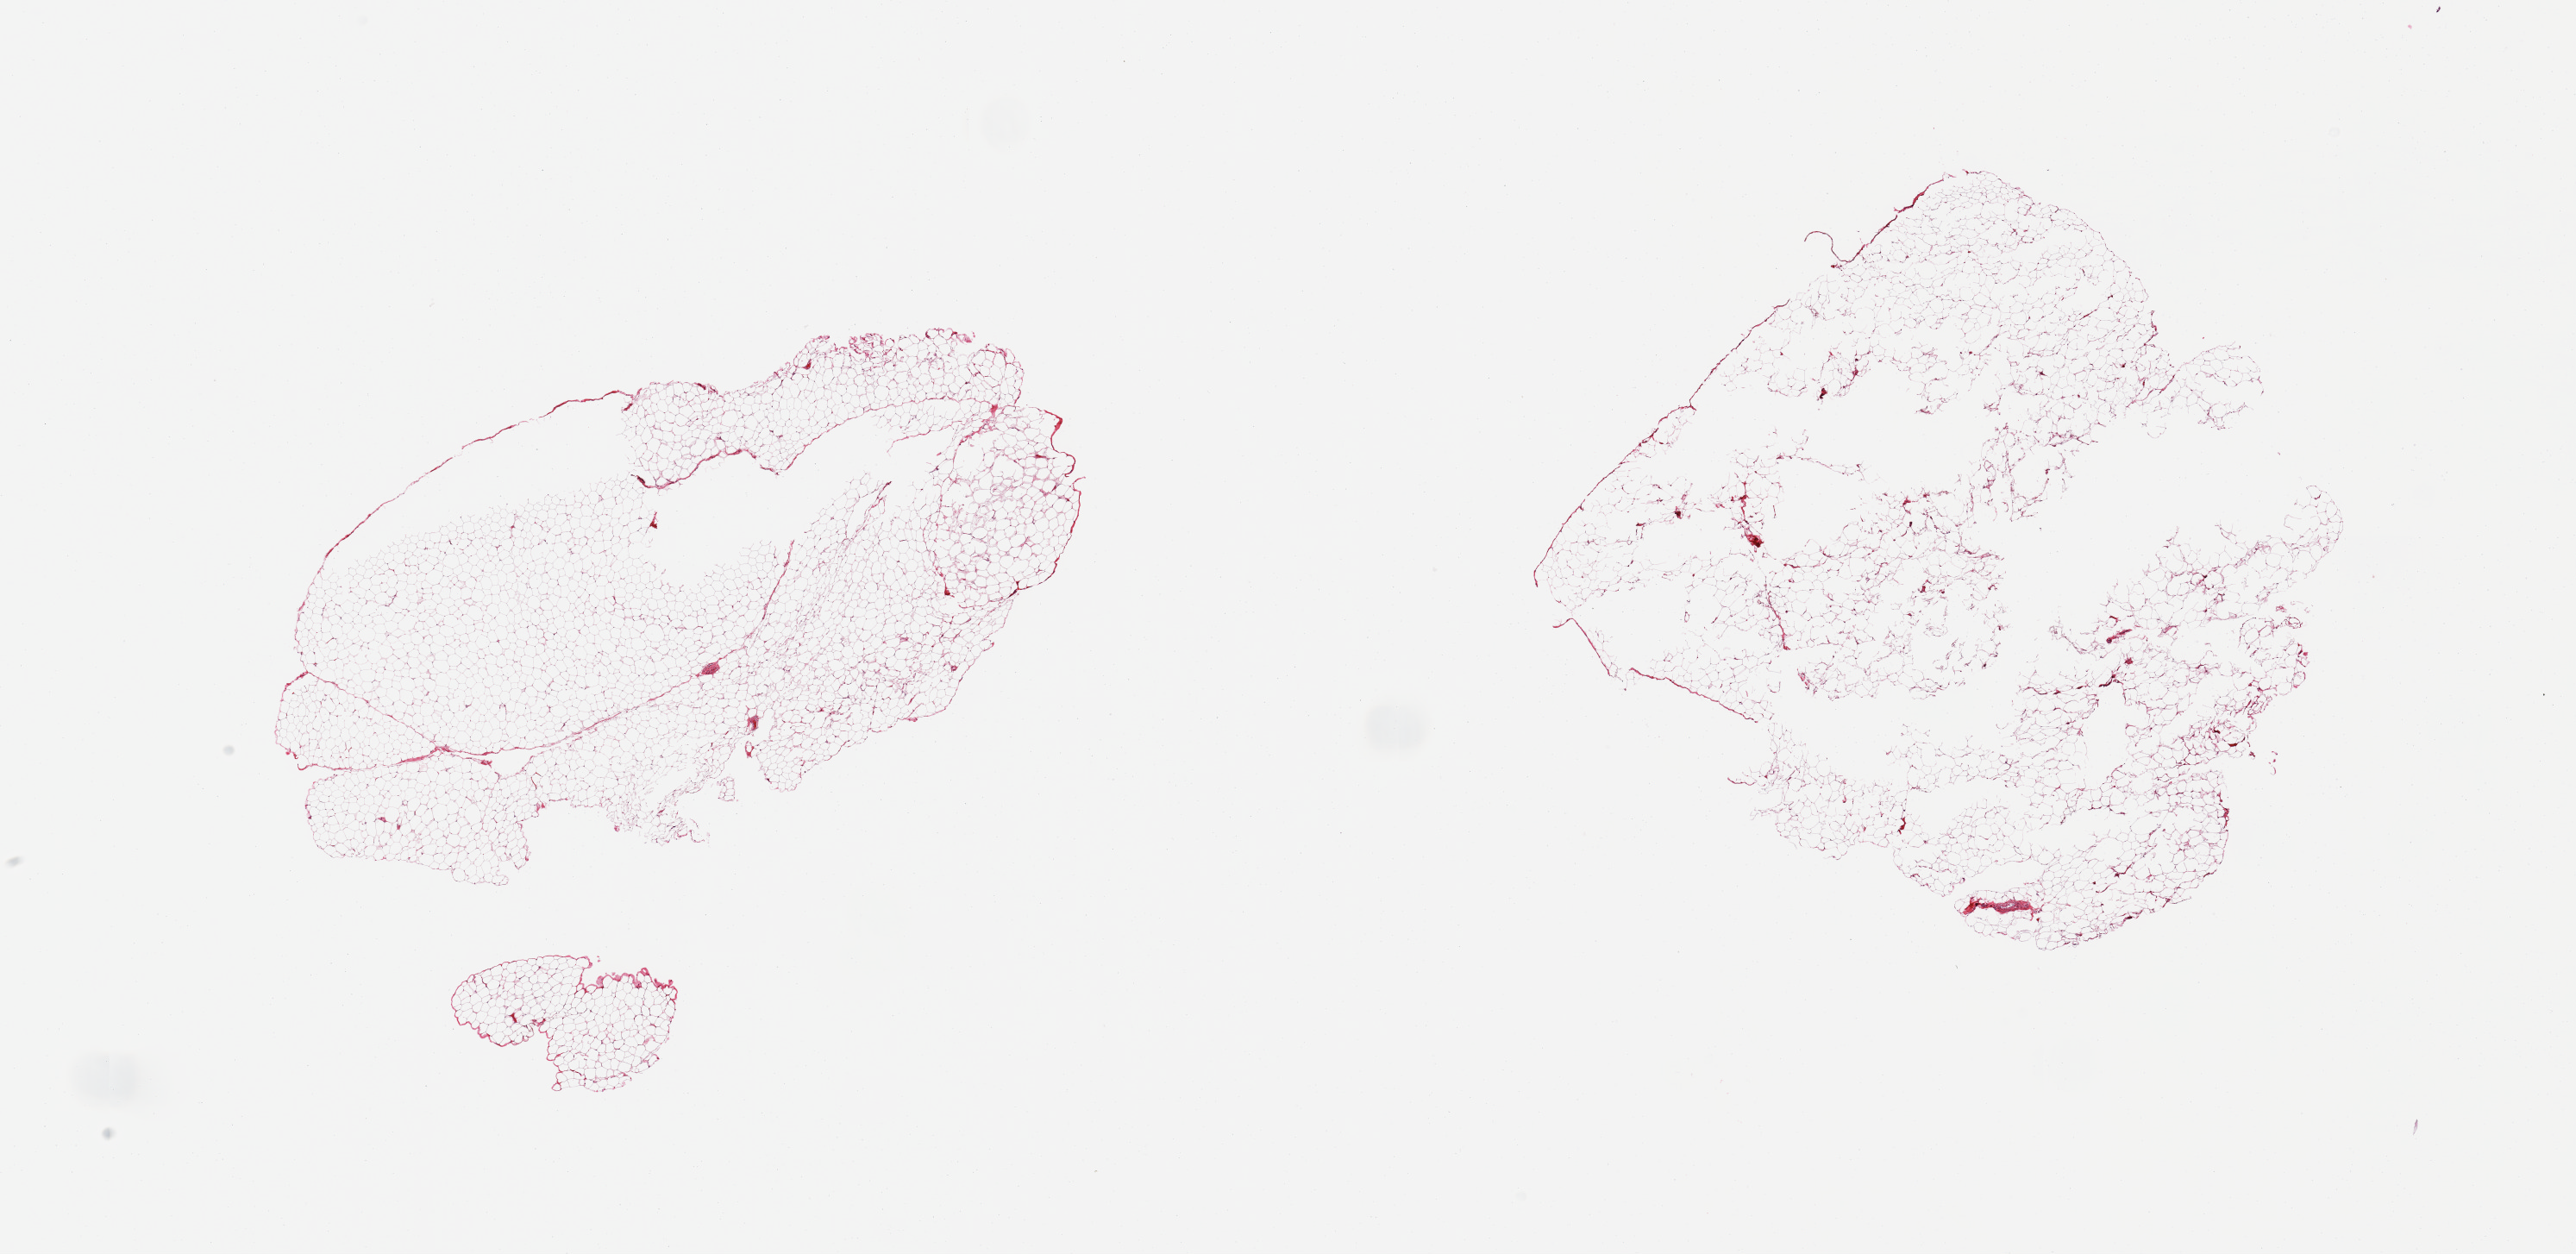
Digitized H&E-stained section, brightfield — low-resolution overview of the scanned area, about 23.6 x 11.5 mm (acquisition: 20x scan). PAXgene-fixed, paraffin-embedded tissue. Section of omentum (target tissue). Tissue donor sample. Donor: male.
Pathologist's review note for this sample: 2 pieces; mature adipose tissue, few central defects (? adequate fixation).